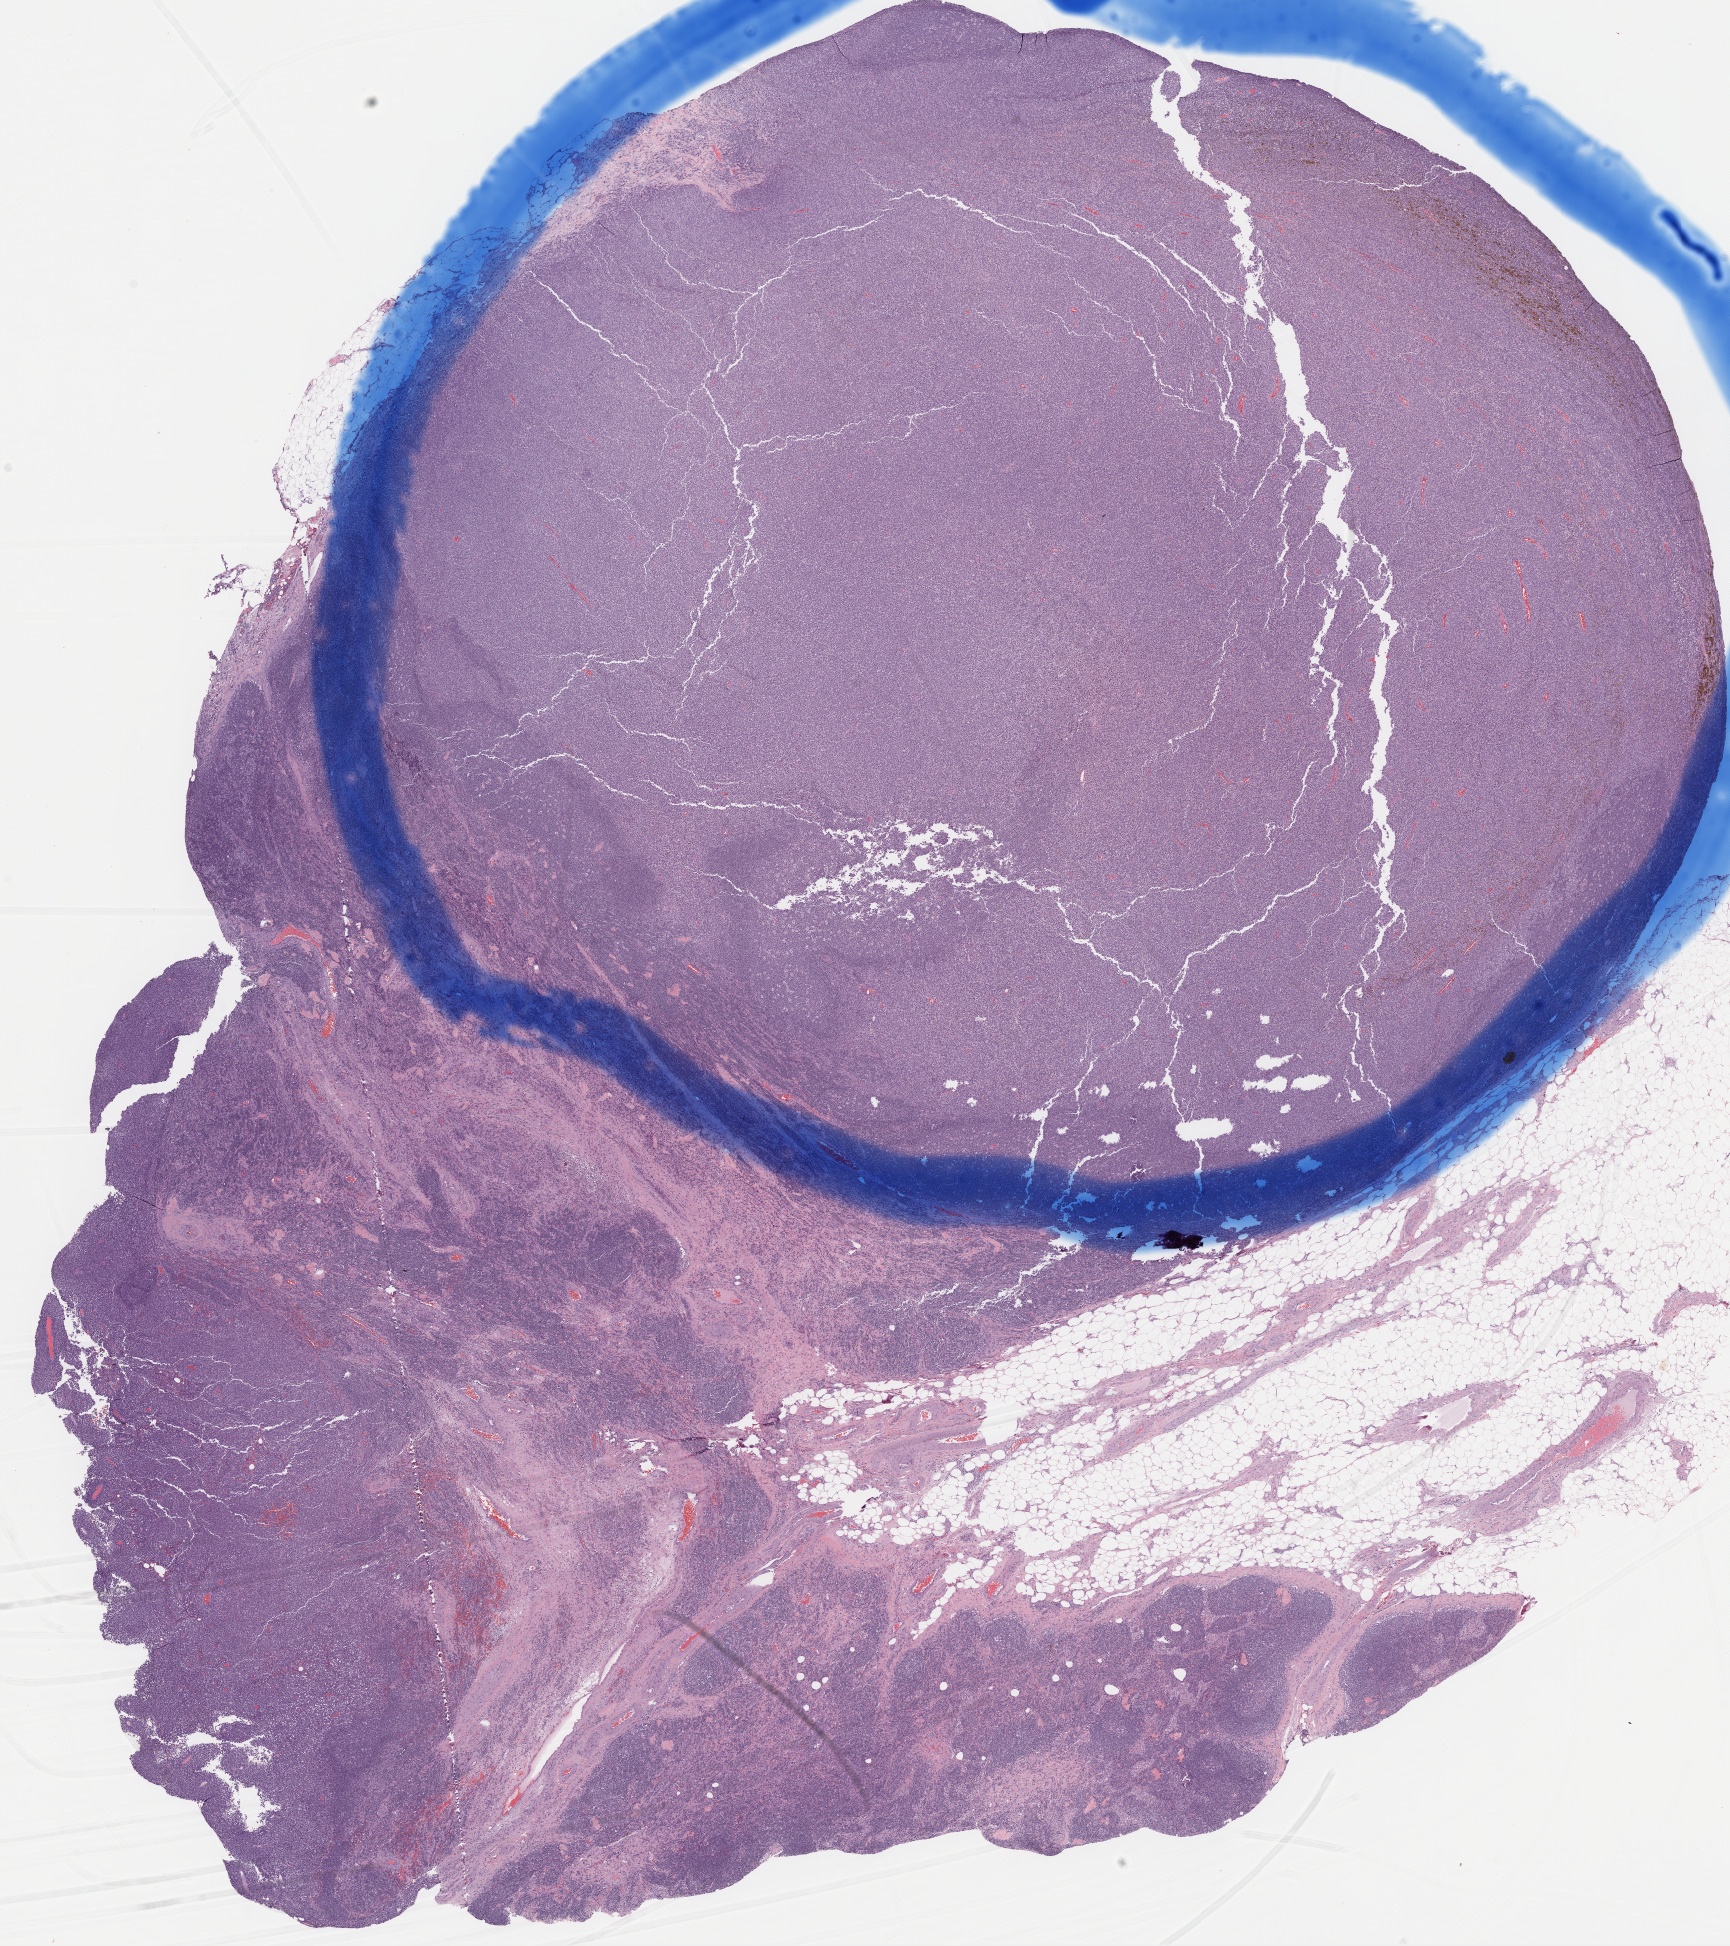
Hematoxylin and eosin (H&E) stained whole-slide image — a low-resolution overview of the entire scanned area, about 14.0 x 15.7 mm; formalin-fixed paraffin-embedded (FFPE) diagnostic section; metastatic tumour sample, sampled site not recorded. Male, age 19 years at initial diagnosis.
* this section: metastatic tumour tissue
* patient diagnosis: Malignant melanoma, NOS